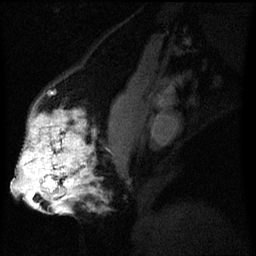
Breast MRI (dynamic contrast-enhanced), one sagittal slice; position 25 of 60 along the scan axis; dynamic contrast-enhanced series, image 2 of 3 at this slice position (ordered by acquisition); 1.5 T; TE 4.2 ms, TR 8 ms; 256 × 256 image matrix. Patient: female, 50 years.
Annotated regions visible in this slice (semi-automatic segmentation, software-assisted and operator-edited):
- analysis volume of interest (the breast-tissue region the enhancement analysis was run in; not a lesion): bounding box <19,112,97,211> (left, top, right, bottom; pixels)
- tumour enhancement mask (voxels above the 70 % enhancement threshold inside the analysis volume of interest): <19,122,89,211>